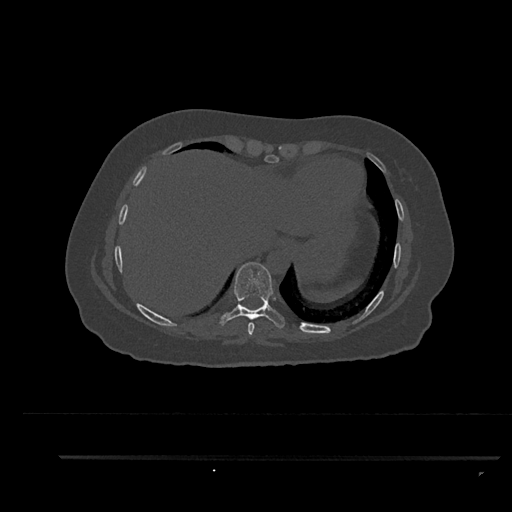
CT including the spine, one axial slice. Position 419 of 797 along the scan axis. Bone window (W 1800 / L 400 HU). 0.5 mm slice thickness. 512 × 512 image matrix, field of view 408 × 408 mm. Patient: female, 44 years. From the clinical record (not read from this slice): primary cancer: renal; vertebrae with lytic lesions (as recorded): L1.
Annotated regions visible in this slice (semi-automatically segmented with operator editing):
- T8 vertebra: box from (x=248, y=322) to (x=255, y=337) px
- T9 vertebra: (x=219, y=262)–(x=285, y=329)